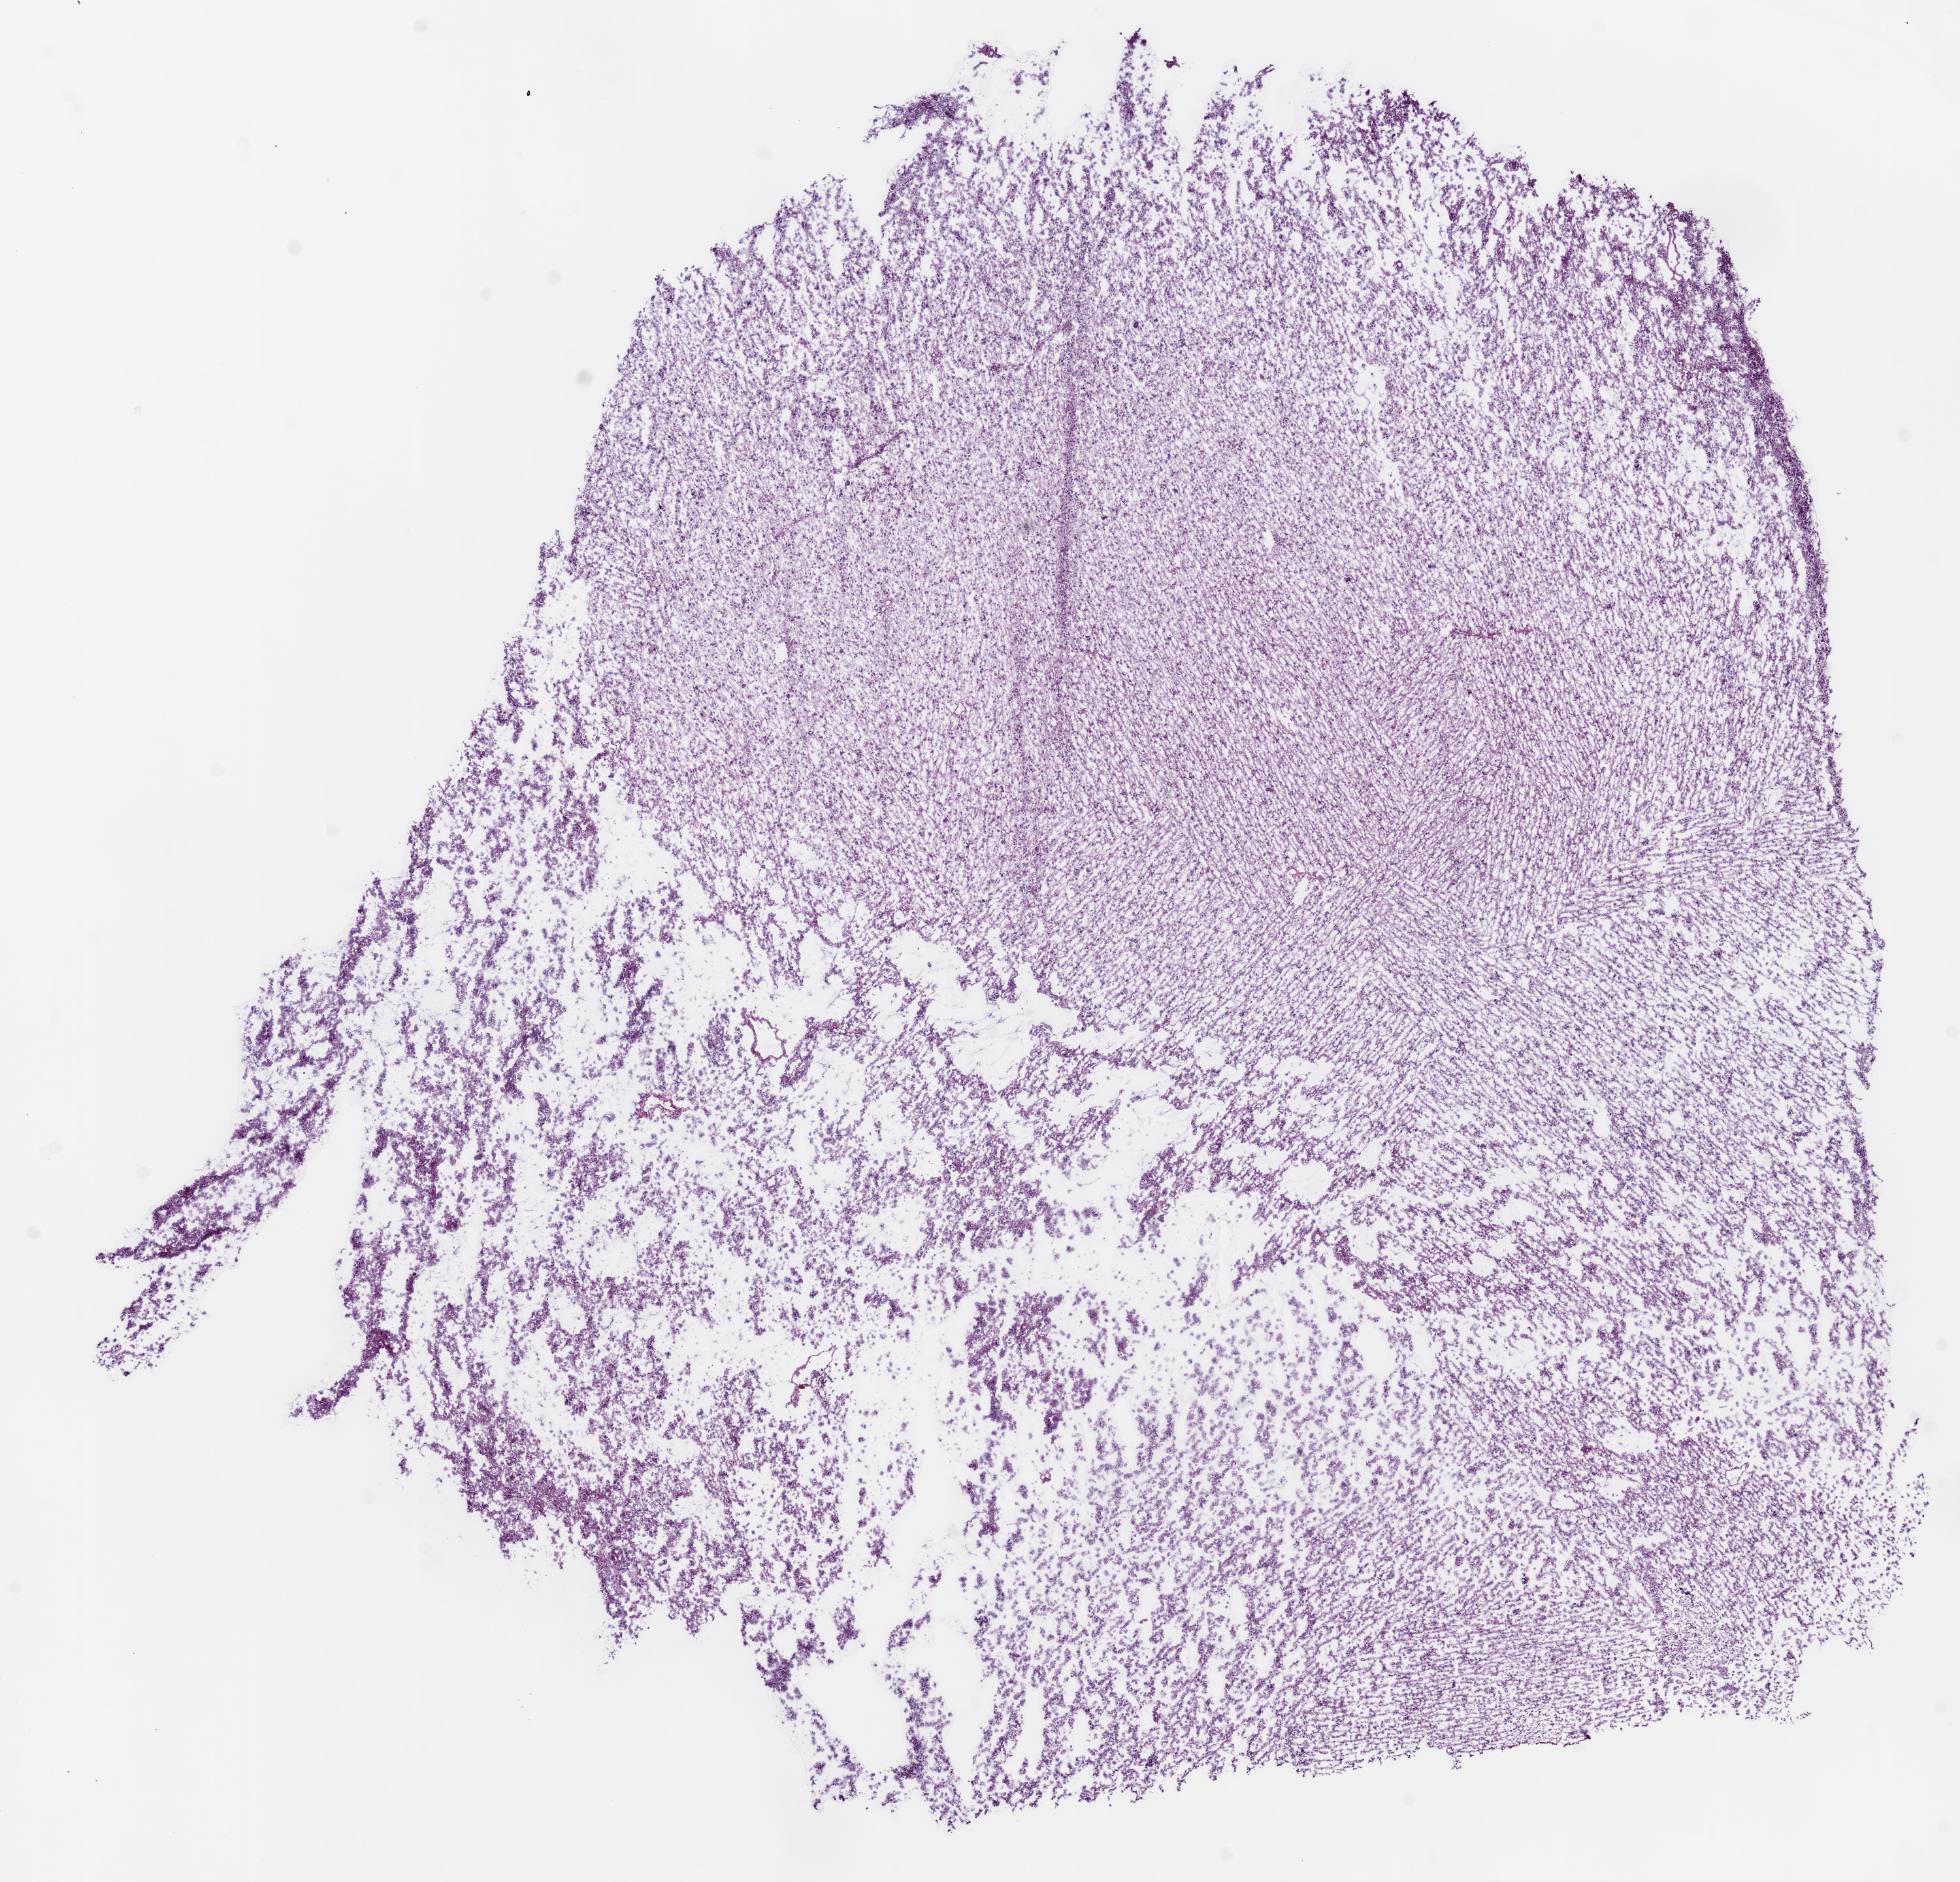
Hematoxylin and eosin (H&E) stained whole-slide image — whole scanned area (about 12.0 x 11.6 mm) shown as a low-resolution overview, frozen section from the bottom of the tissue portion, brain, primary tumour sample. Male patient; age at initial diagnosis 34 years. Histologic grade: G3 (poorly differentiated). Pathologist review of this section (percent, as recorded): tumour cells 100%, tumour nuclei 65%, normal cells 0%, stromal cells 0%, necrosis 0%.
* histologic diagnosis: Astrocytoma, anaplastic (cerebrum)